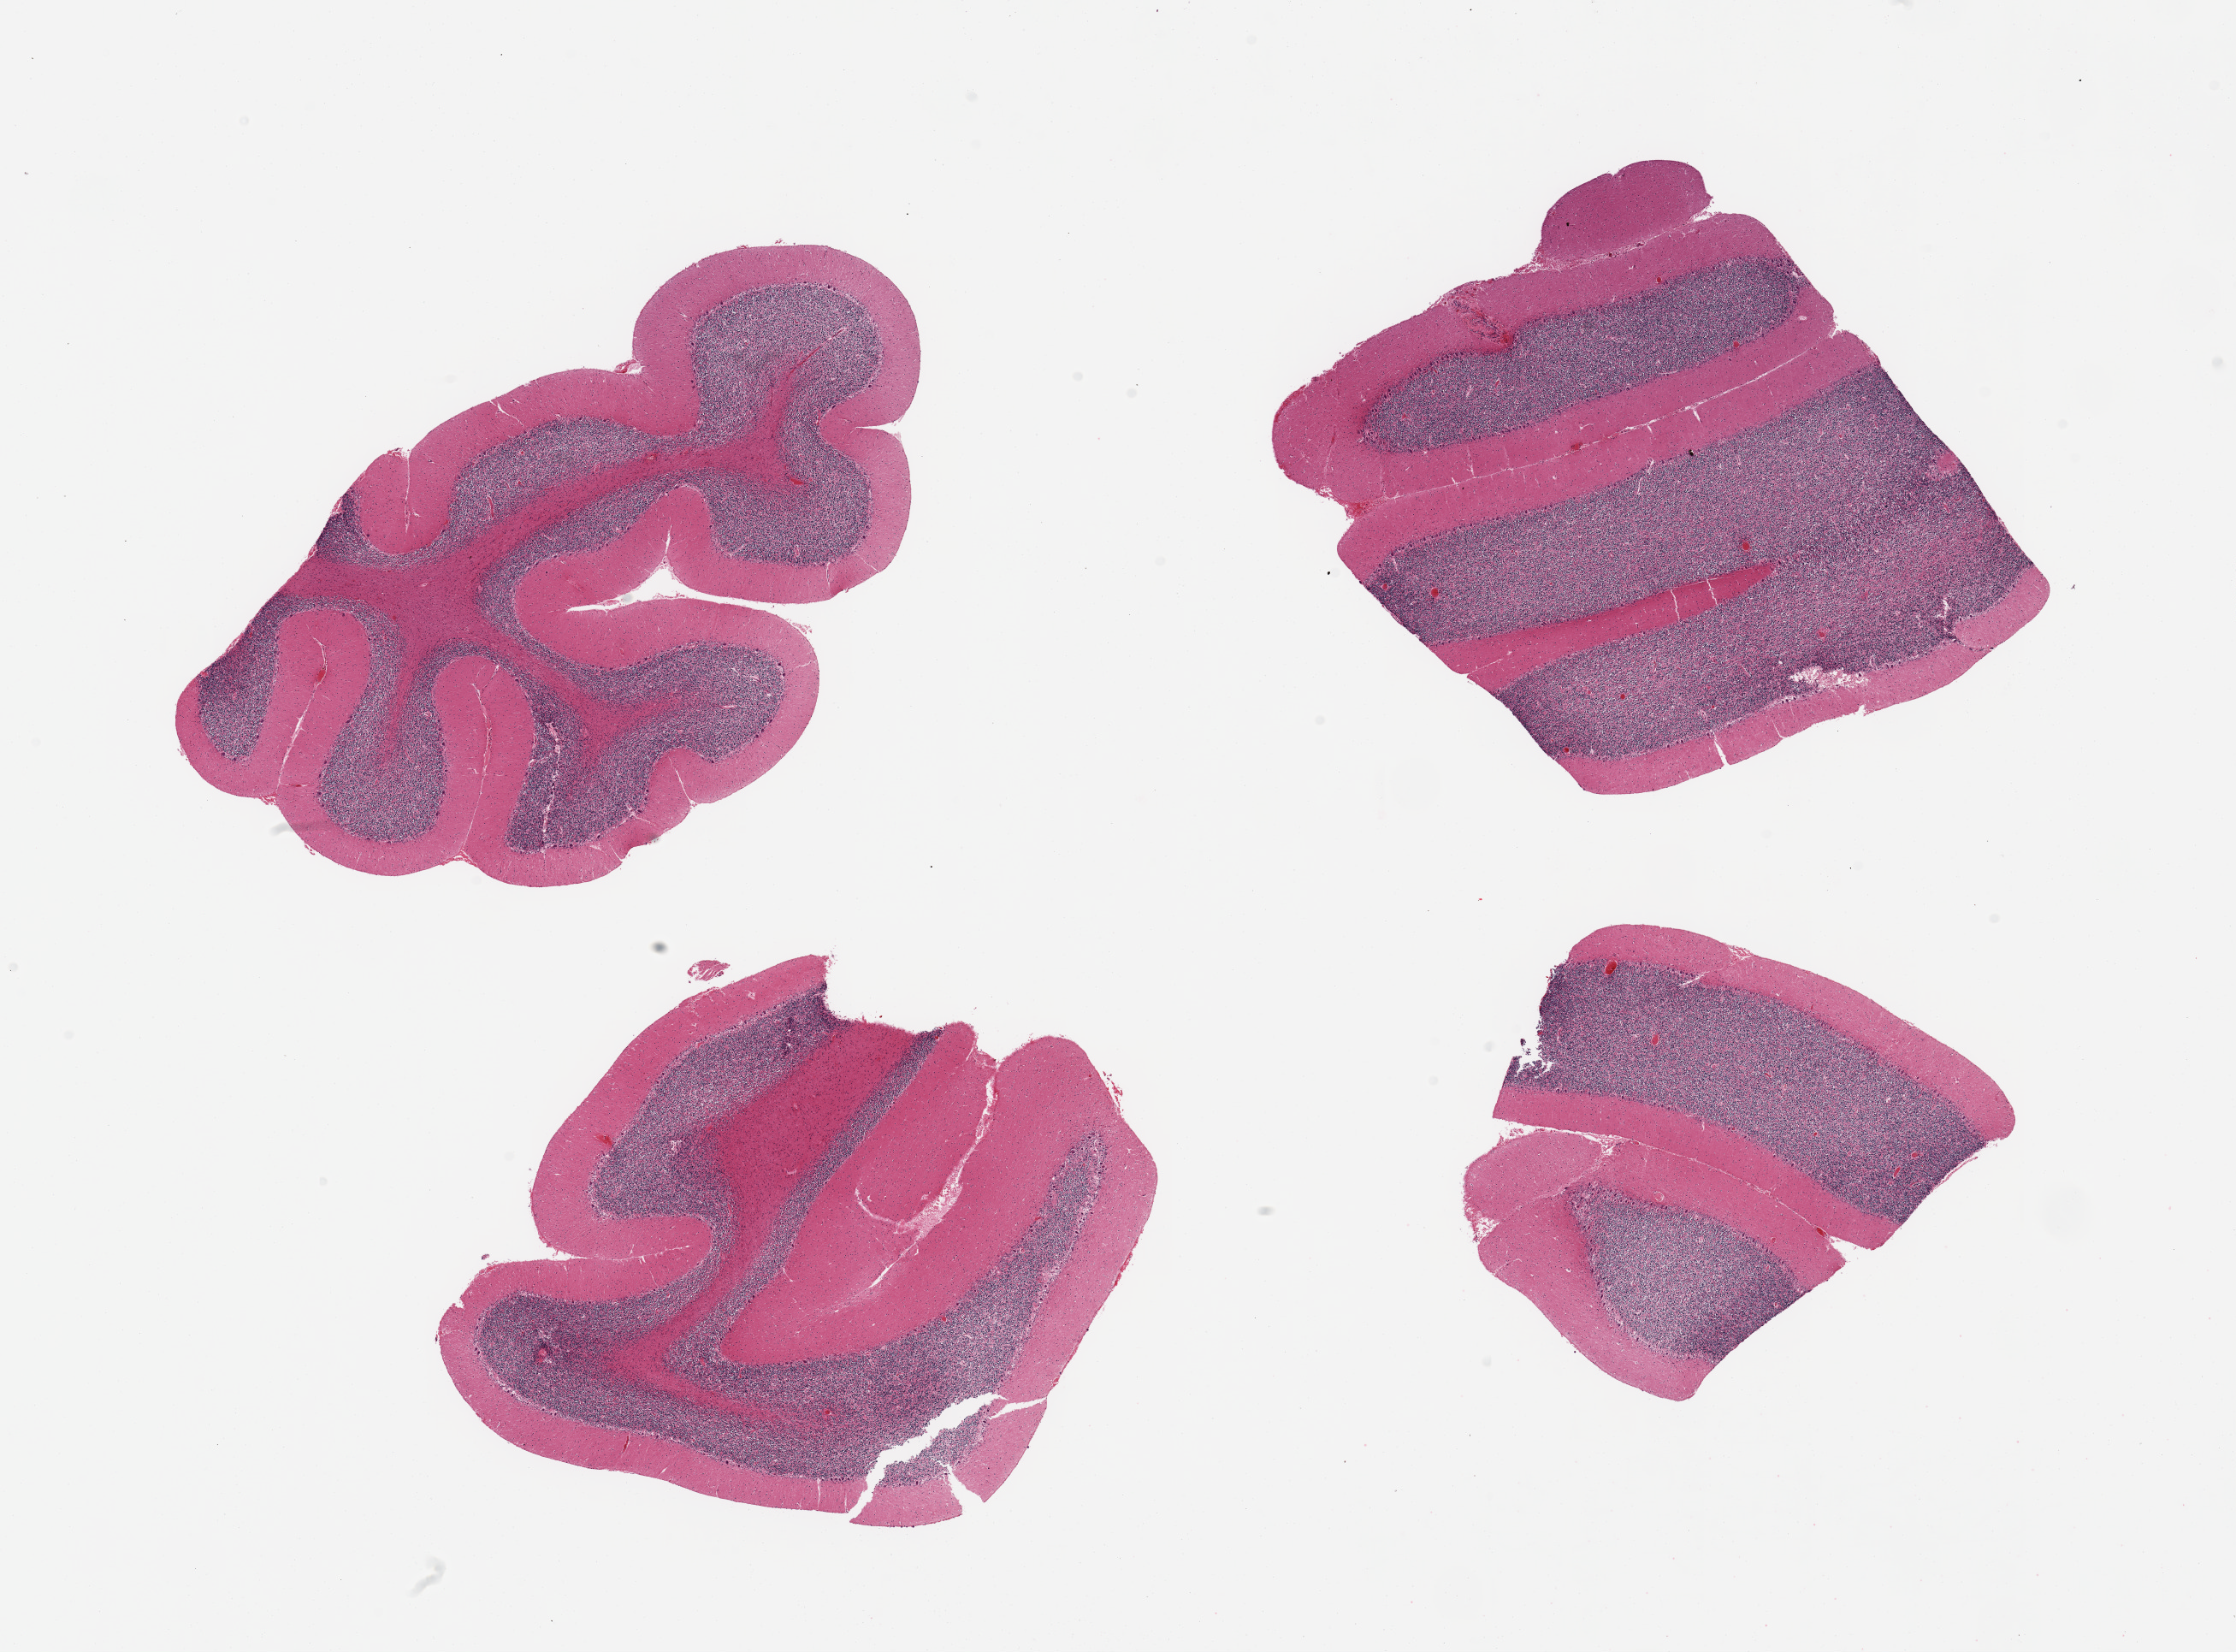
Hematoxylin and eosin (H&E) whole-slide image — a low-resolution overview of the entire scanned area, about 20.7 x 15.3 mm. PAXgene-fixed paraffin-embedded (PFPE) section. Section of cerebellum (target tissue). Tissue donor sample.
* pathologist's review note for this sample: 4 pieces